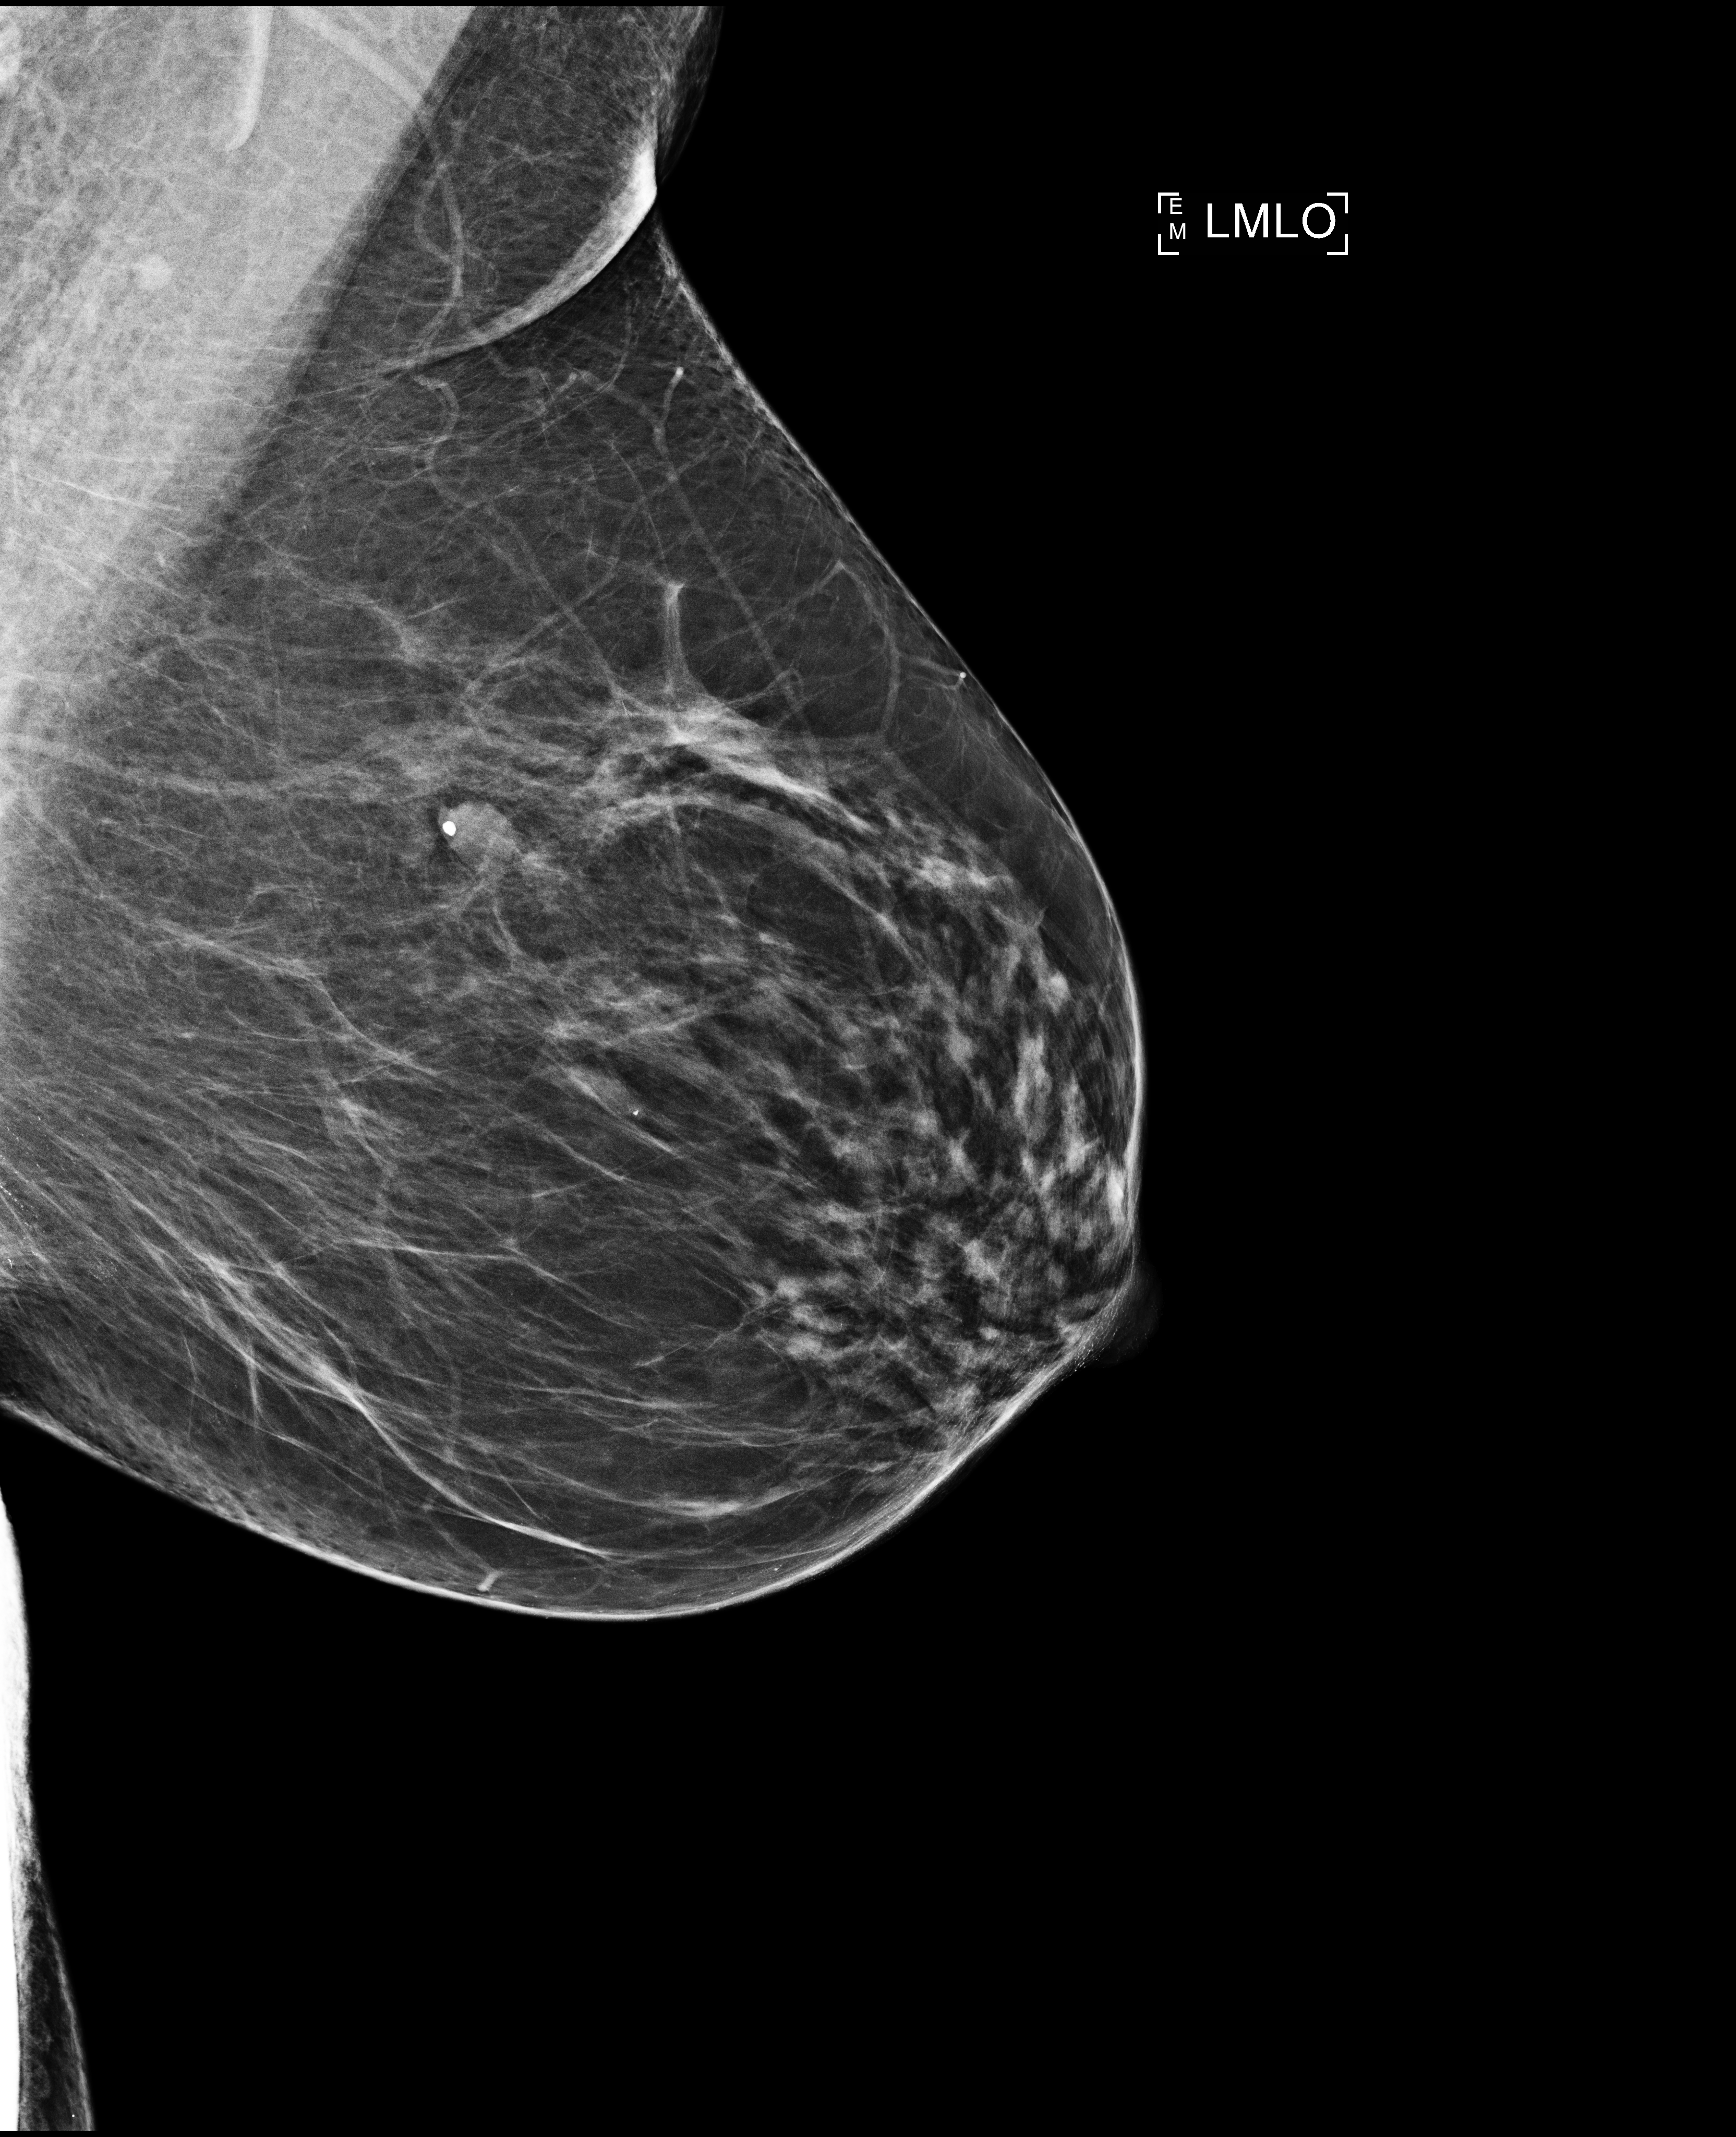
Full-field digital mammogram (FFDM); left breast; MLO view; annual screening mammography examination; compressed breast thickness 70 mm. Female patient, age 64 years.
Breast density at the screening exam (both breasts): scattered fibroglandular densities (BI-RADS density category b). Final BI-RADS assessment for this screening round (tomosynthesis exam, both breasts): category 2. Recall: no recall after this screen.